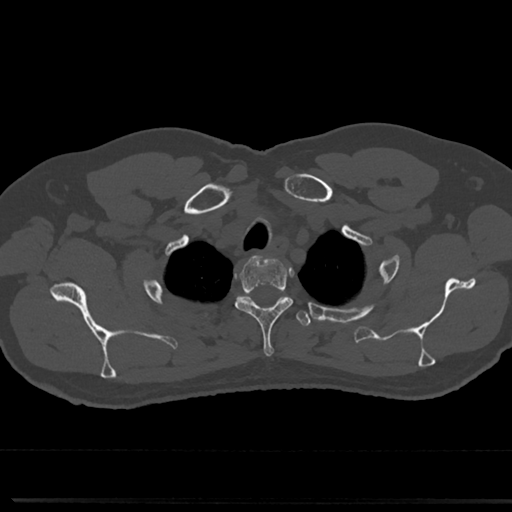
CT including the spine, one axial slice; position 627 of 817 along the scan axis; reconstruction kernel Br40s/3; 120 kVp; bone window (W 1800 / L 400 HU); 0.5 mm slice thickness; 512 × 512 image matrix, field of view 355 × 355 mm. Patient: male, 61 years. Case-level facts recorded for this patient, not image findings: primary cancer: prostate.
Structures marked on this image (semi-automatic segmentation, software-assisted and operator-edited):
- T1 vertebra: bounding box (x1, y1, x2, y2) in pixels: (239, 296, 287, 305)
- T2 vertebra: (235, 254, 292, 357)
- T3 vertebra: (243, 297, 311, 328)